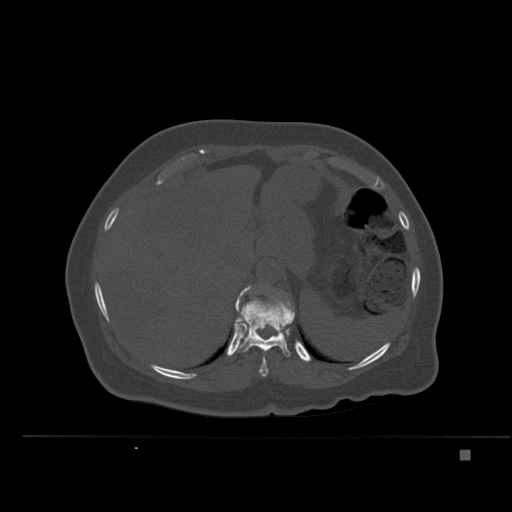
CT including the spine, one axial slice; position 269 of 477 along the scan axis; bone window (W 1800 / L 400 HU); 1.5 mm slice thickness; 512 × 512 image matrix. Female patient, age 74 years. Case-level facts recorded for this patient, not image findings: primary cancer: colon.
Annotated regions visible in this slice (semi-automatically segmented with operator editing):
- T10 vertebra: bounding box [x1, y1, x2, y2] px = [259, 357, 268, 377]
- T11 vertebra: [235, 289, 295, 357]
- T12 vertebra: [235, 285, 289, 307]